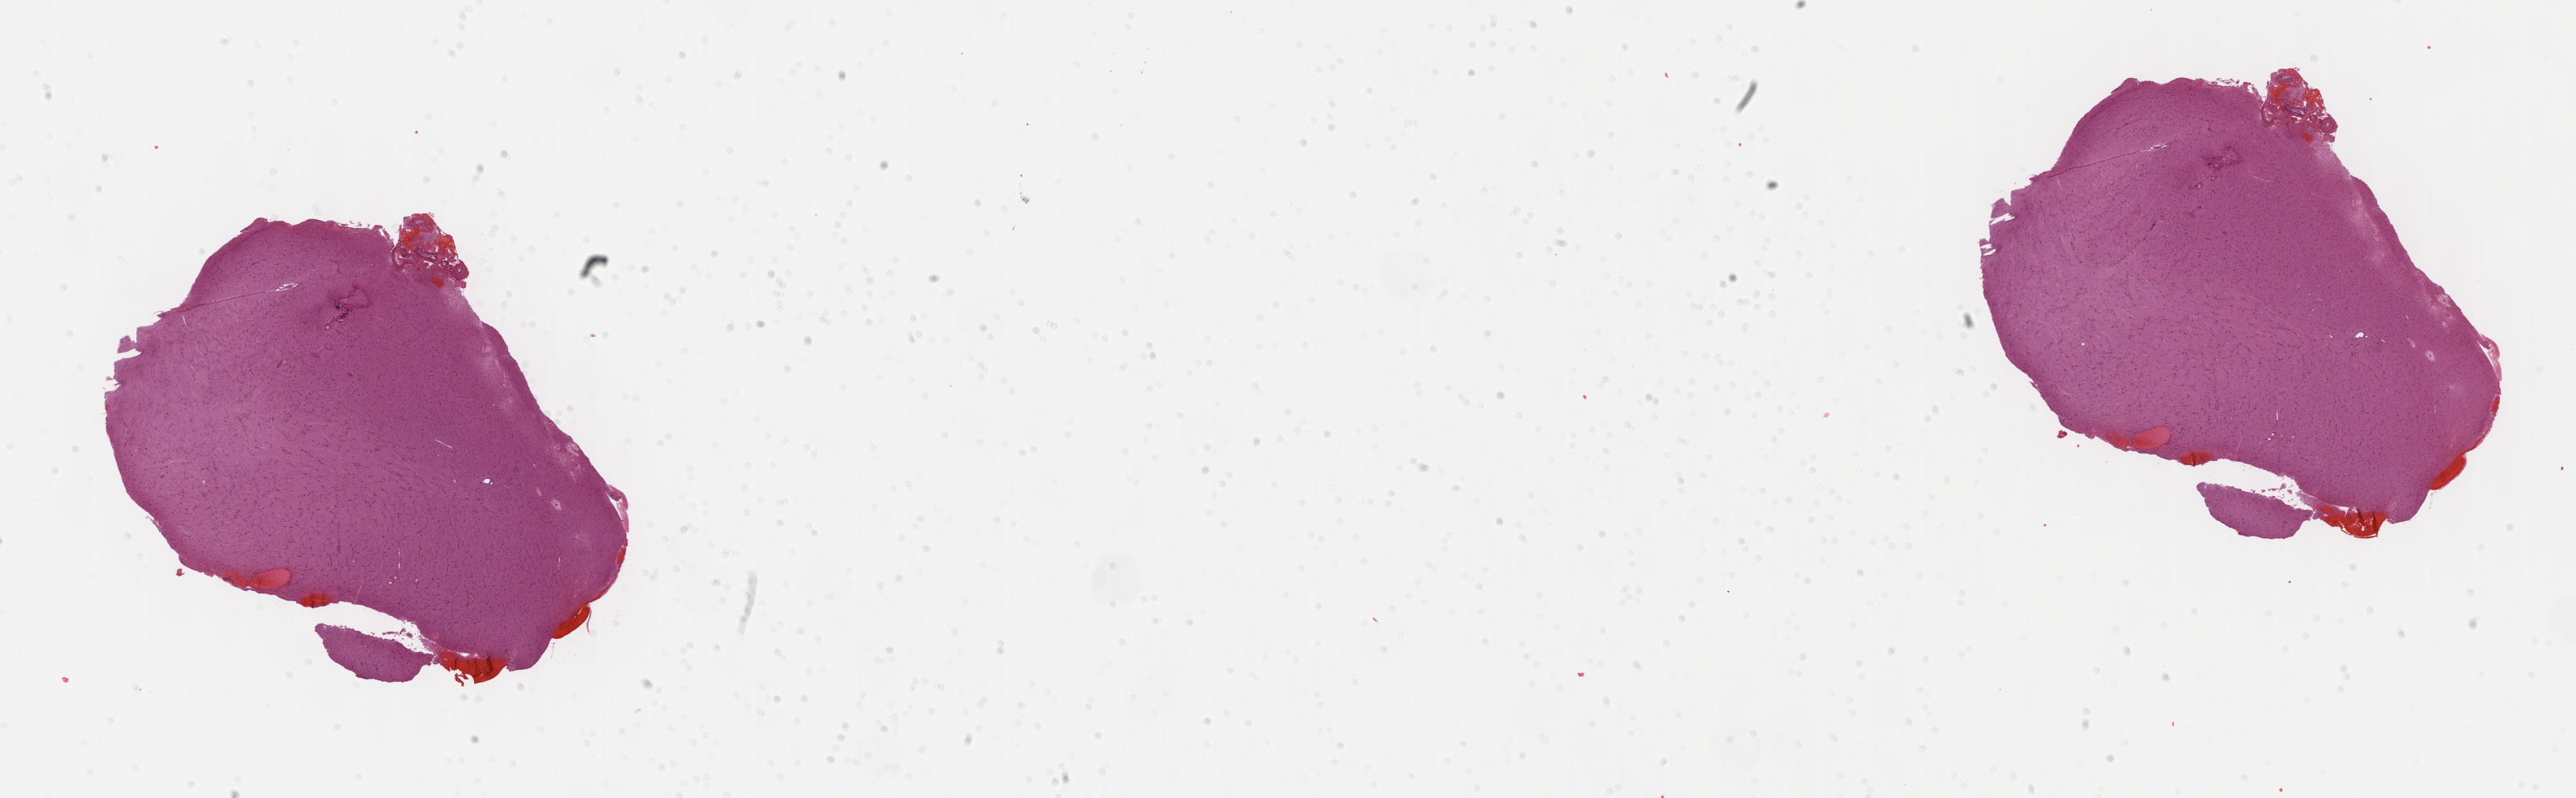
Hematoxylin and eosin (H&E) stained whole-slide image, a low-resolution overview of the entire scanned area, about 25.7 x 8.0 mm (from a 40x scan); formalin-fixed paraffin-embedded (FFPE) diagnostic section; sample: primary tumour, brain. Female, age 18 years at initial diagnosis. Histologic grade: G2 (moderately differentiated).
- laterality: left
- histologic diagnosis: Mixed glioma